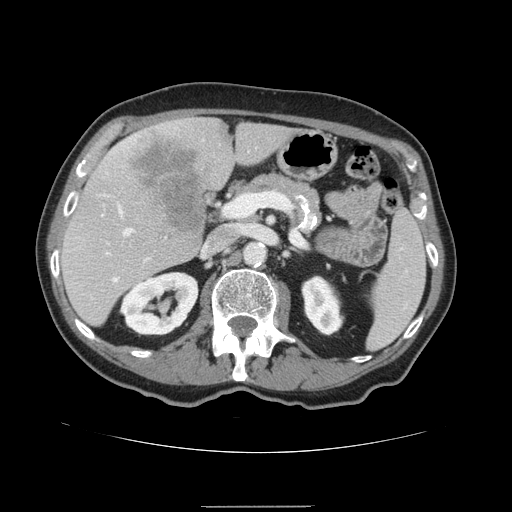
Contrast-enhanced abdominal CT, one axial slice. Slice 81 of 168 in the series (ordered by position). 120 kVp. Intravenous contrast given. Soft-tissue window (W 400 / L 40 HU). 2.5 mm slice thickness. 512 × 512 image matrix, field of view 386 × 386 mm. Male patient, age 74 years. Case-level facts recorded for this patient, not image findings: diagnosis: colorectal cancer liver metastases, imaged before liver resection; multiple liver metastases: no; largest metastasis: 14.5 cm; chemotherapy before resection: no.
Structures marked on this image (expert manual segmentation):
- hepatic veins: bounding box [x1, y1, x2, y2] px = [115, 206, 133, 280]
- liver: [61, 117, 297, 327]
- planned liver remnant (the part of the liver to remain after resection): [61, 123, 298, 327]
- portal vein (with intrahepatic branches): [105, 199, 240, 268]
- liver metastasis: [127, 135, 212, 235]